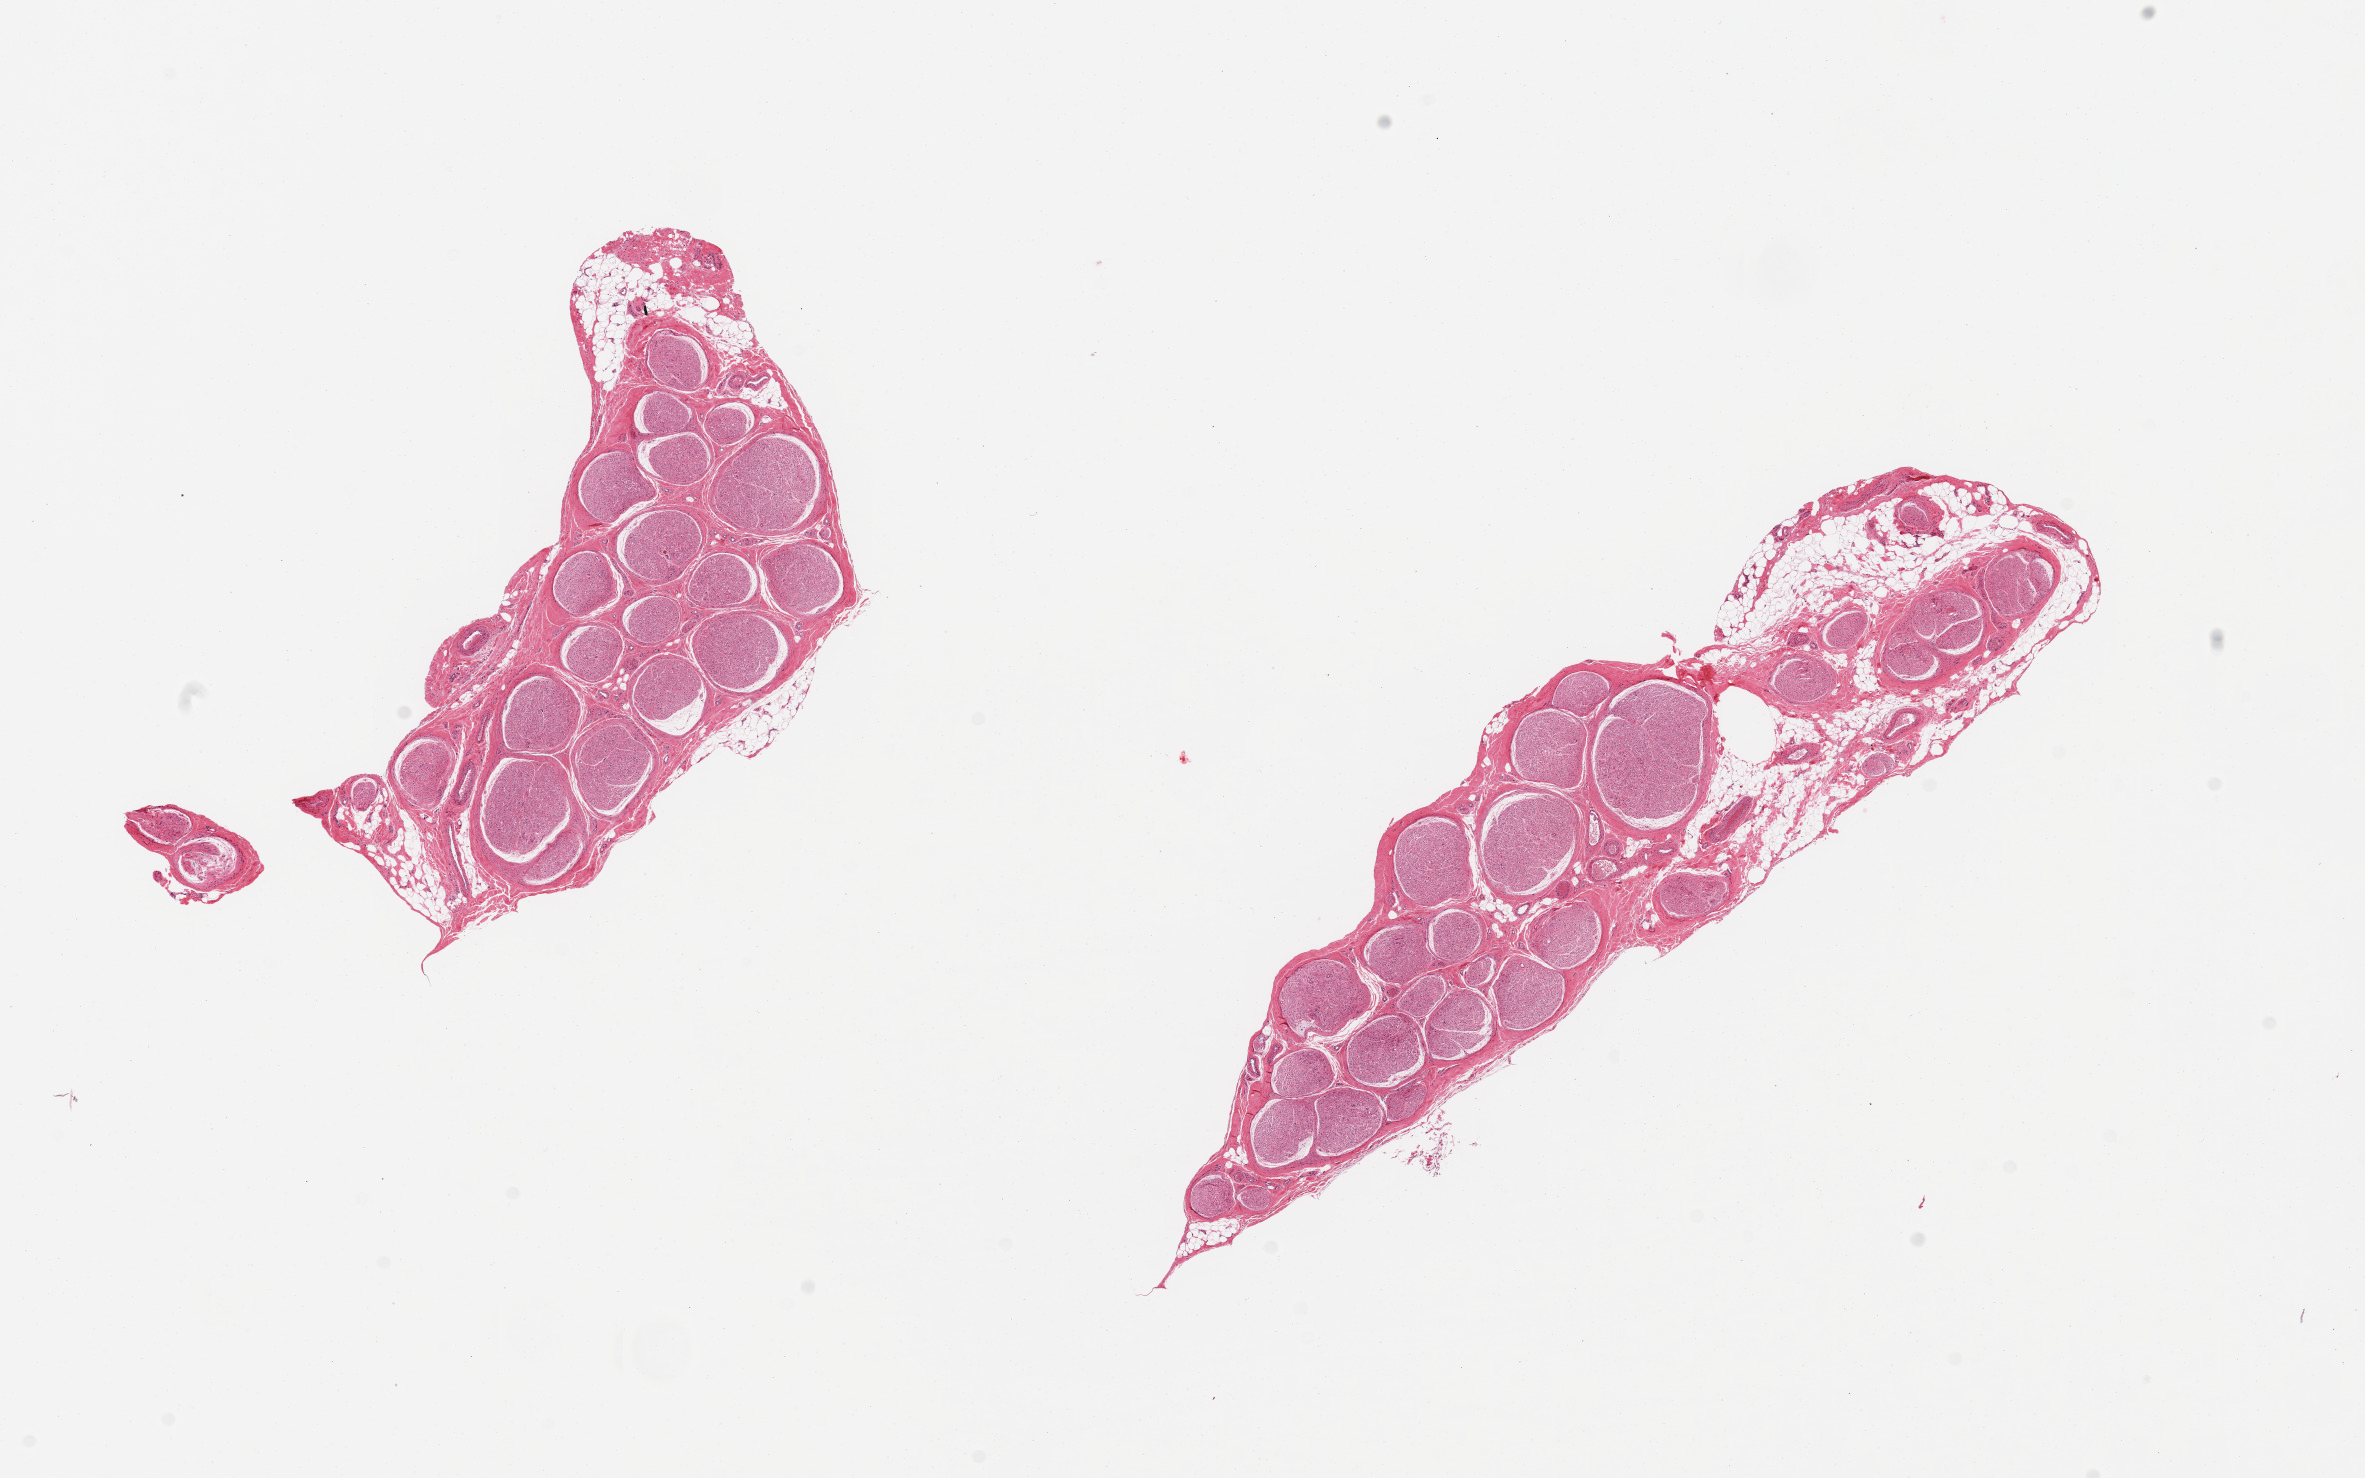
Whole-slide image, H&E stain — whole scanned area (about 18.7 x 11.7 mm) shown as a low-resolution overview, PAXgene-fixed paraffin-embedded (PFPE) section, target tissue: tibial nerve, donor tissue sample.
- reviewer comment on this tissue sample: 2 pieces; 10% internal & external fat